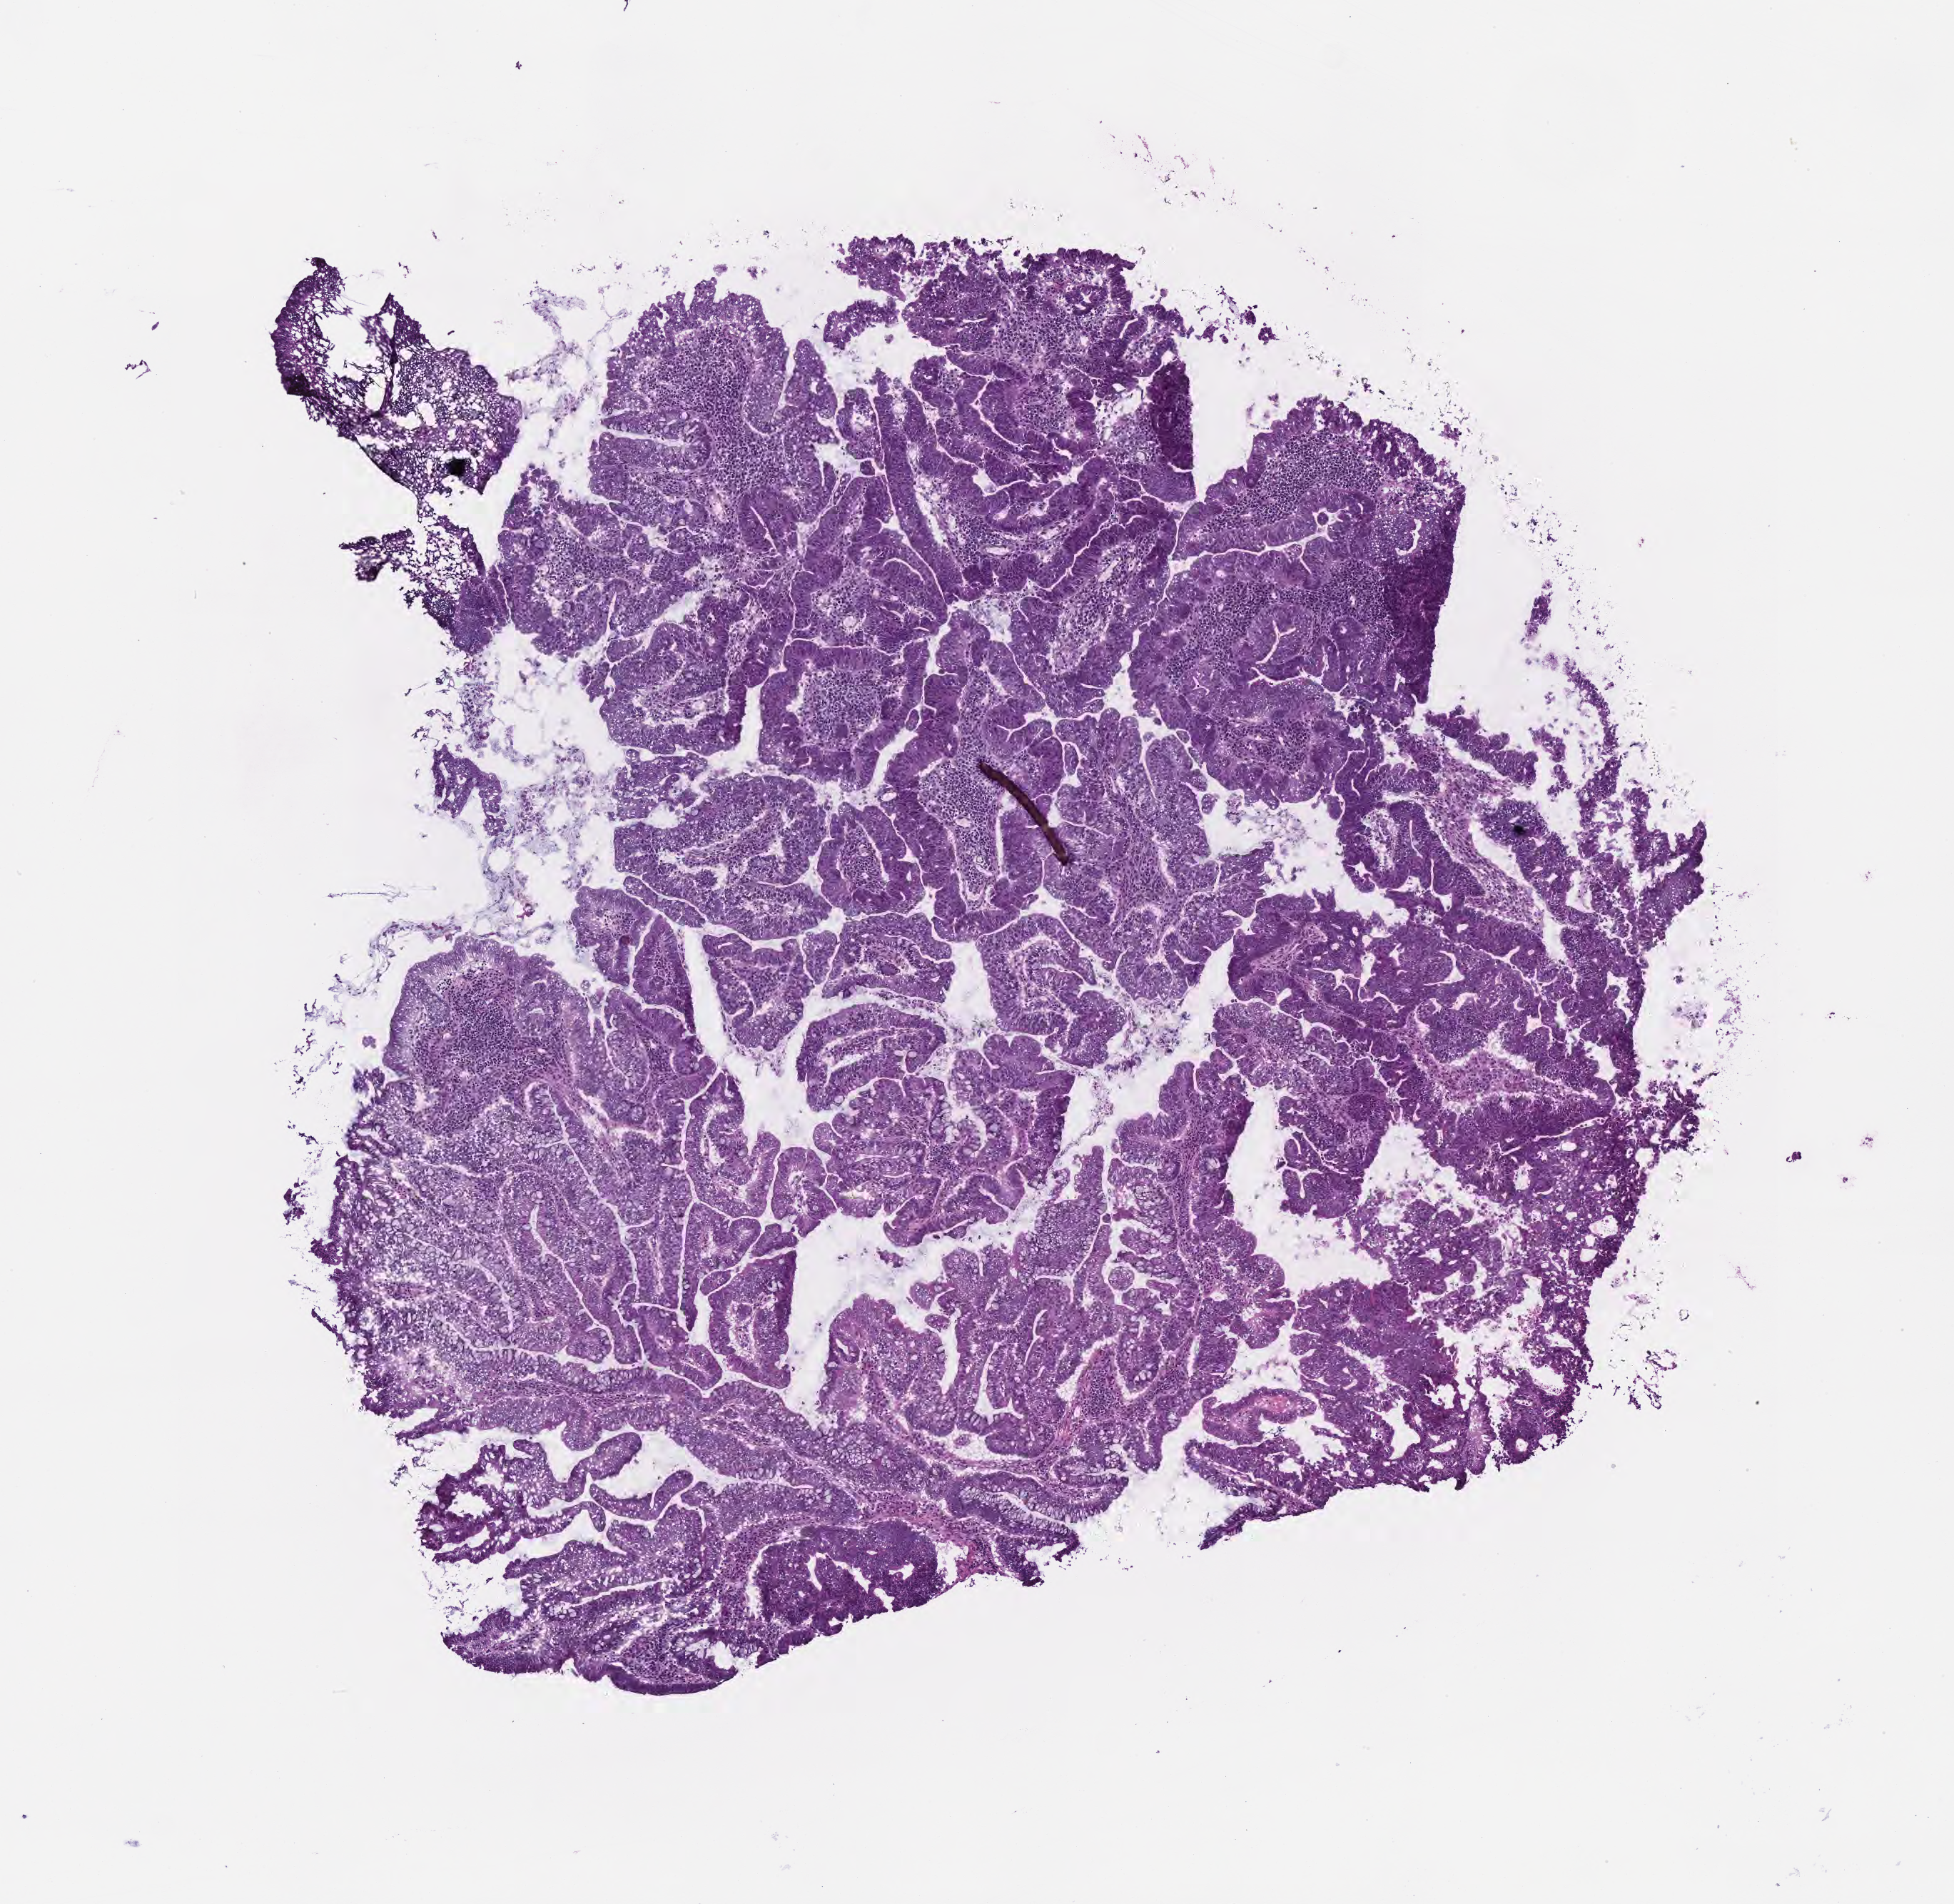
Haematoxylin and eosin whole-slide image — low-resolution overview of the scanned area, about 5.5 x 5.4 mm. Frozen section (tissue freezing medium). Specimen: primary tumor. Site: rectum. Female patient. Tumor grade: G2 (moderately differentiated). Slide review estimates, as recorded: tumor cells 100%, tumor nuclei 70%, stromal cells 0%, necrosis 0%, normal cells 0%. Infiltration values recorded for this section: lymphocyte infiltration 0%, monocyte infiltration 0%, neutrophil infiltration 0%.
* AJCC pathologic stage: Stage I
* diagnosis: Adenocarcinoma, NOS